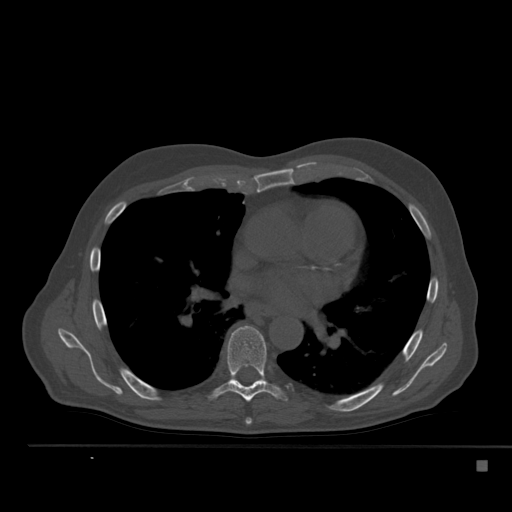
CT including the spine, one axial slice; position 328 of 517 along the scan axis; reconstruction kernel Br40s; bone window (W 1800 / L 400 HU); 512 × 512 image matrix, field of view 408 × 408 mm. Male patient, age 70 years. Case-level facts recorded for this patient, not image findings: primary cancer: renal.
Structures marked on this image (semi-automatically segmented with operator editing):
- T6 vertebra: bounding box (x1, y1, x2, y2) in pixels: (245, 418, 252, 425)
- T7 vertebra: (210, 326, 287, 402)